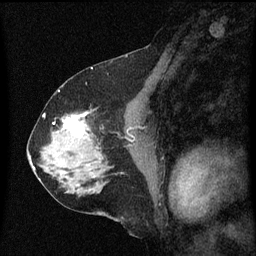
Breast MRI (dynamic contrast-enhanced), one sagittal slice; position 33 of 60 along the scan axis; dynamic contrast-enhanced series, image 2 of 3 at this slice position (ordered by acquisition); 1.5 T; TE 4.2 ms, TR 8 ms; 2 mm slice thickness; 256 × 256 image matrix. Patient: female, 58 years.
Structures marked on this image (semi-automatic segmentation, software-assisted and operator-edited):
- analysis volume of interest (the breast-tissue region the enhancement analysis was run in; not a lesion): bounding box (x1, y1, x2, y2) in pixels: (56, 108, 99, 149)
- tumour enhancement mask (voxels above the 70 % enhancement threshold inside the analysis volume of interest): (63, 112, 89, 135)